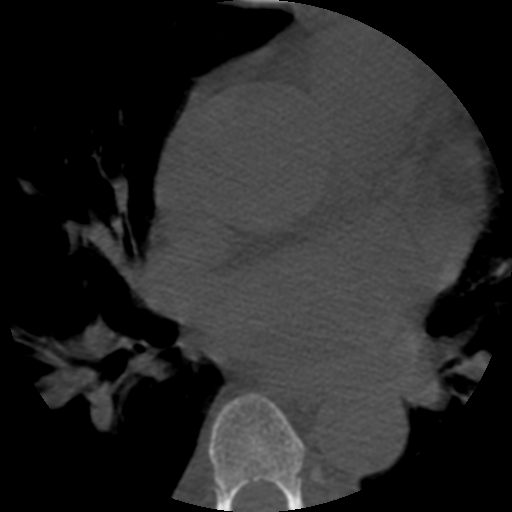
CT including the spine, one axial slice; reconstruction kernel STANDARD; 120 kVp; bone window (W 1800 / L 400 HU); 512 × 512 image matrix, field of view 160 × 160 mm. Patient age 57 years. From the clinical record (not read from this slice): primary cancer: prostate.
Structures marked on this image (semi-automatically segmented with operator editing):
- T6 vertebra: bounding box <209,394,303,512> (left, top, right, bottom; pixels)